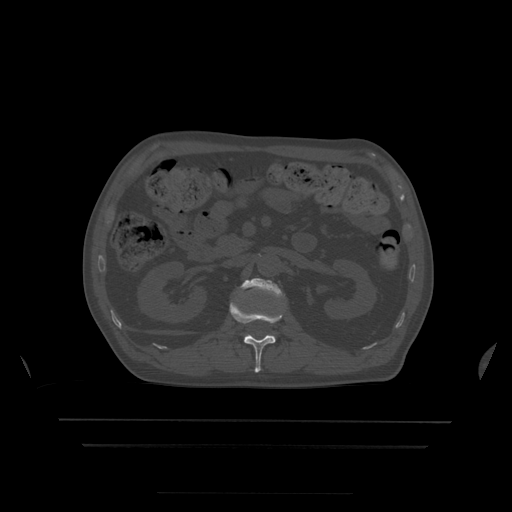
CT including the spine, one axial slice. Position 163 of 522 along the scan axis. Bone window (W 1800 / L 400 HU). 512 × 512 image matrix, field of view 436 × 436 mm. Patient age 68 years. From the clinical record (not read from this slice): primary cancer: urothelial.
Structures marked on this image (semi-automatically segmented with operator editing):
- L1 vertebra: bounding box <230,302,283,373> (left, top, right, bottom; pixels)
- L2 vertebra: <241,278,283,298>